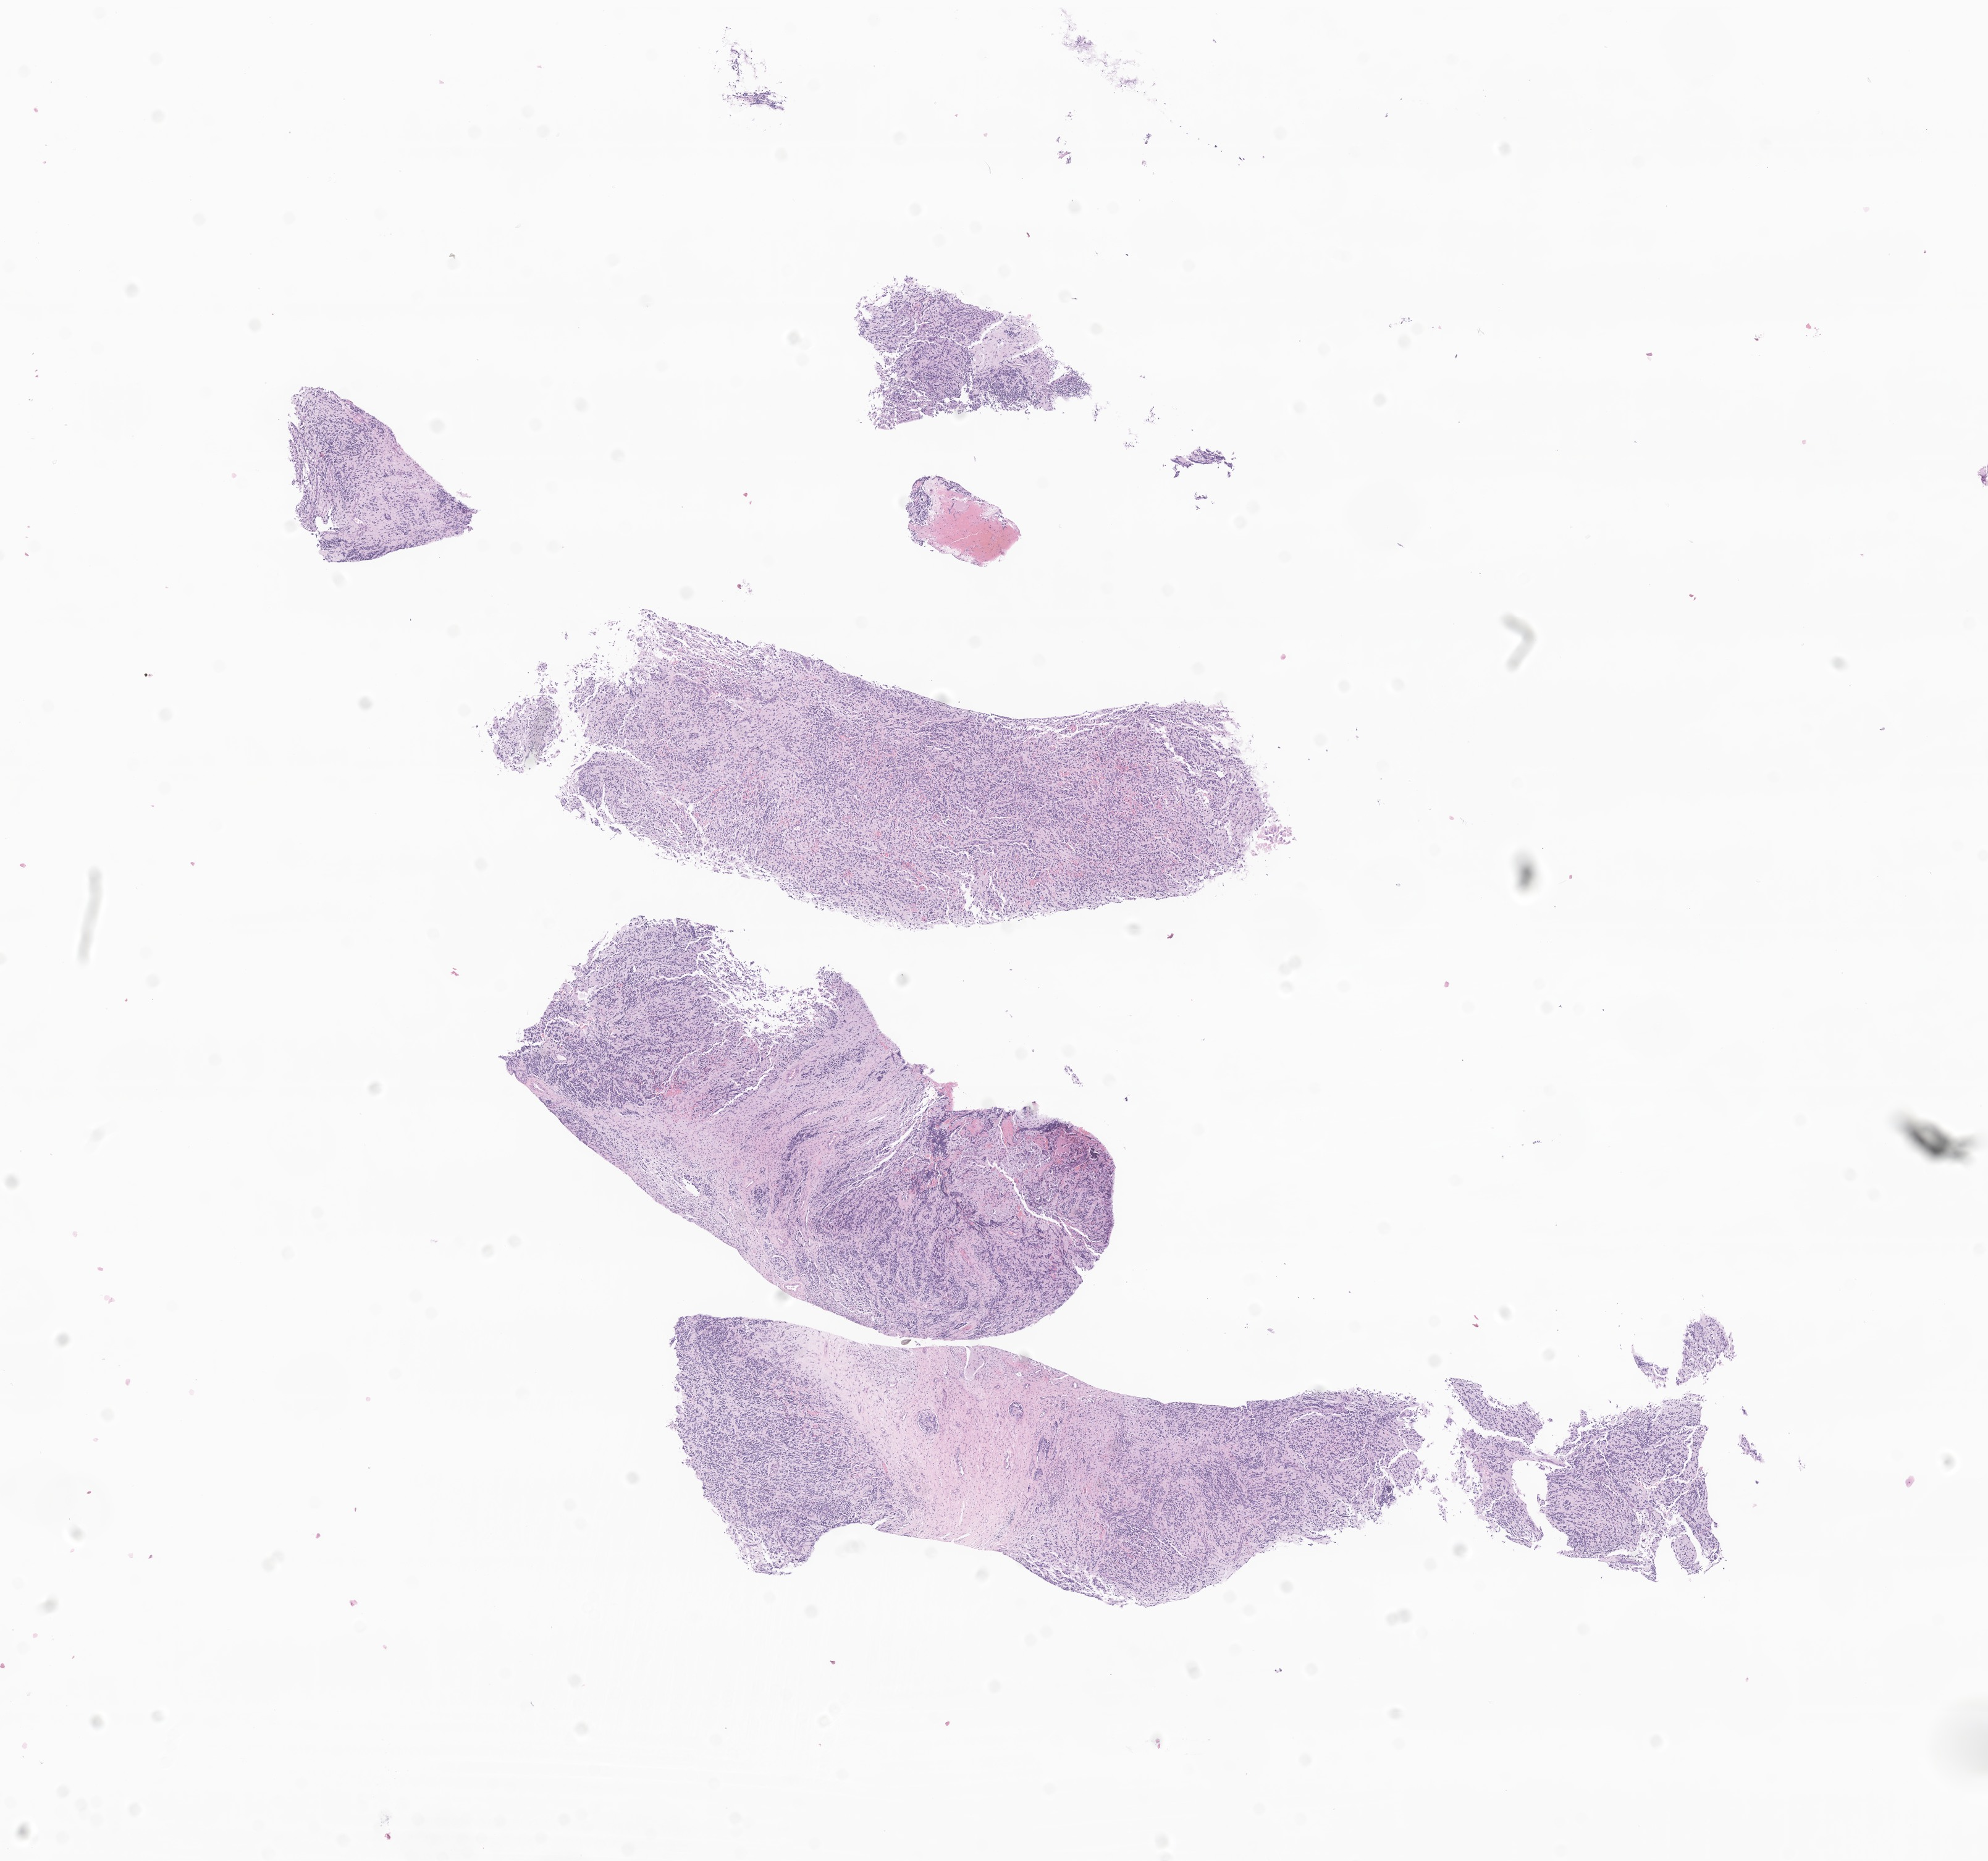
Digitized haematoxylin and eosin-stained section of tumor tissue from the abdomen, whole scanned area (about 13.6 x 12.7 mm) shown as a low-resolution overview; FFPE section. Patient: female, age 651 days (about 1.8 years).
Diagnosis: Neuroblastoma, NOS.